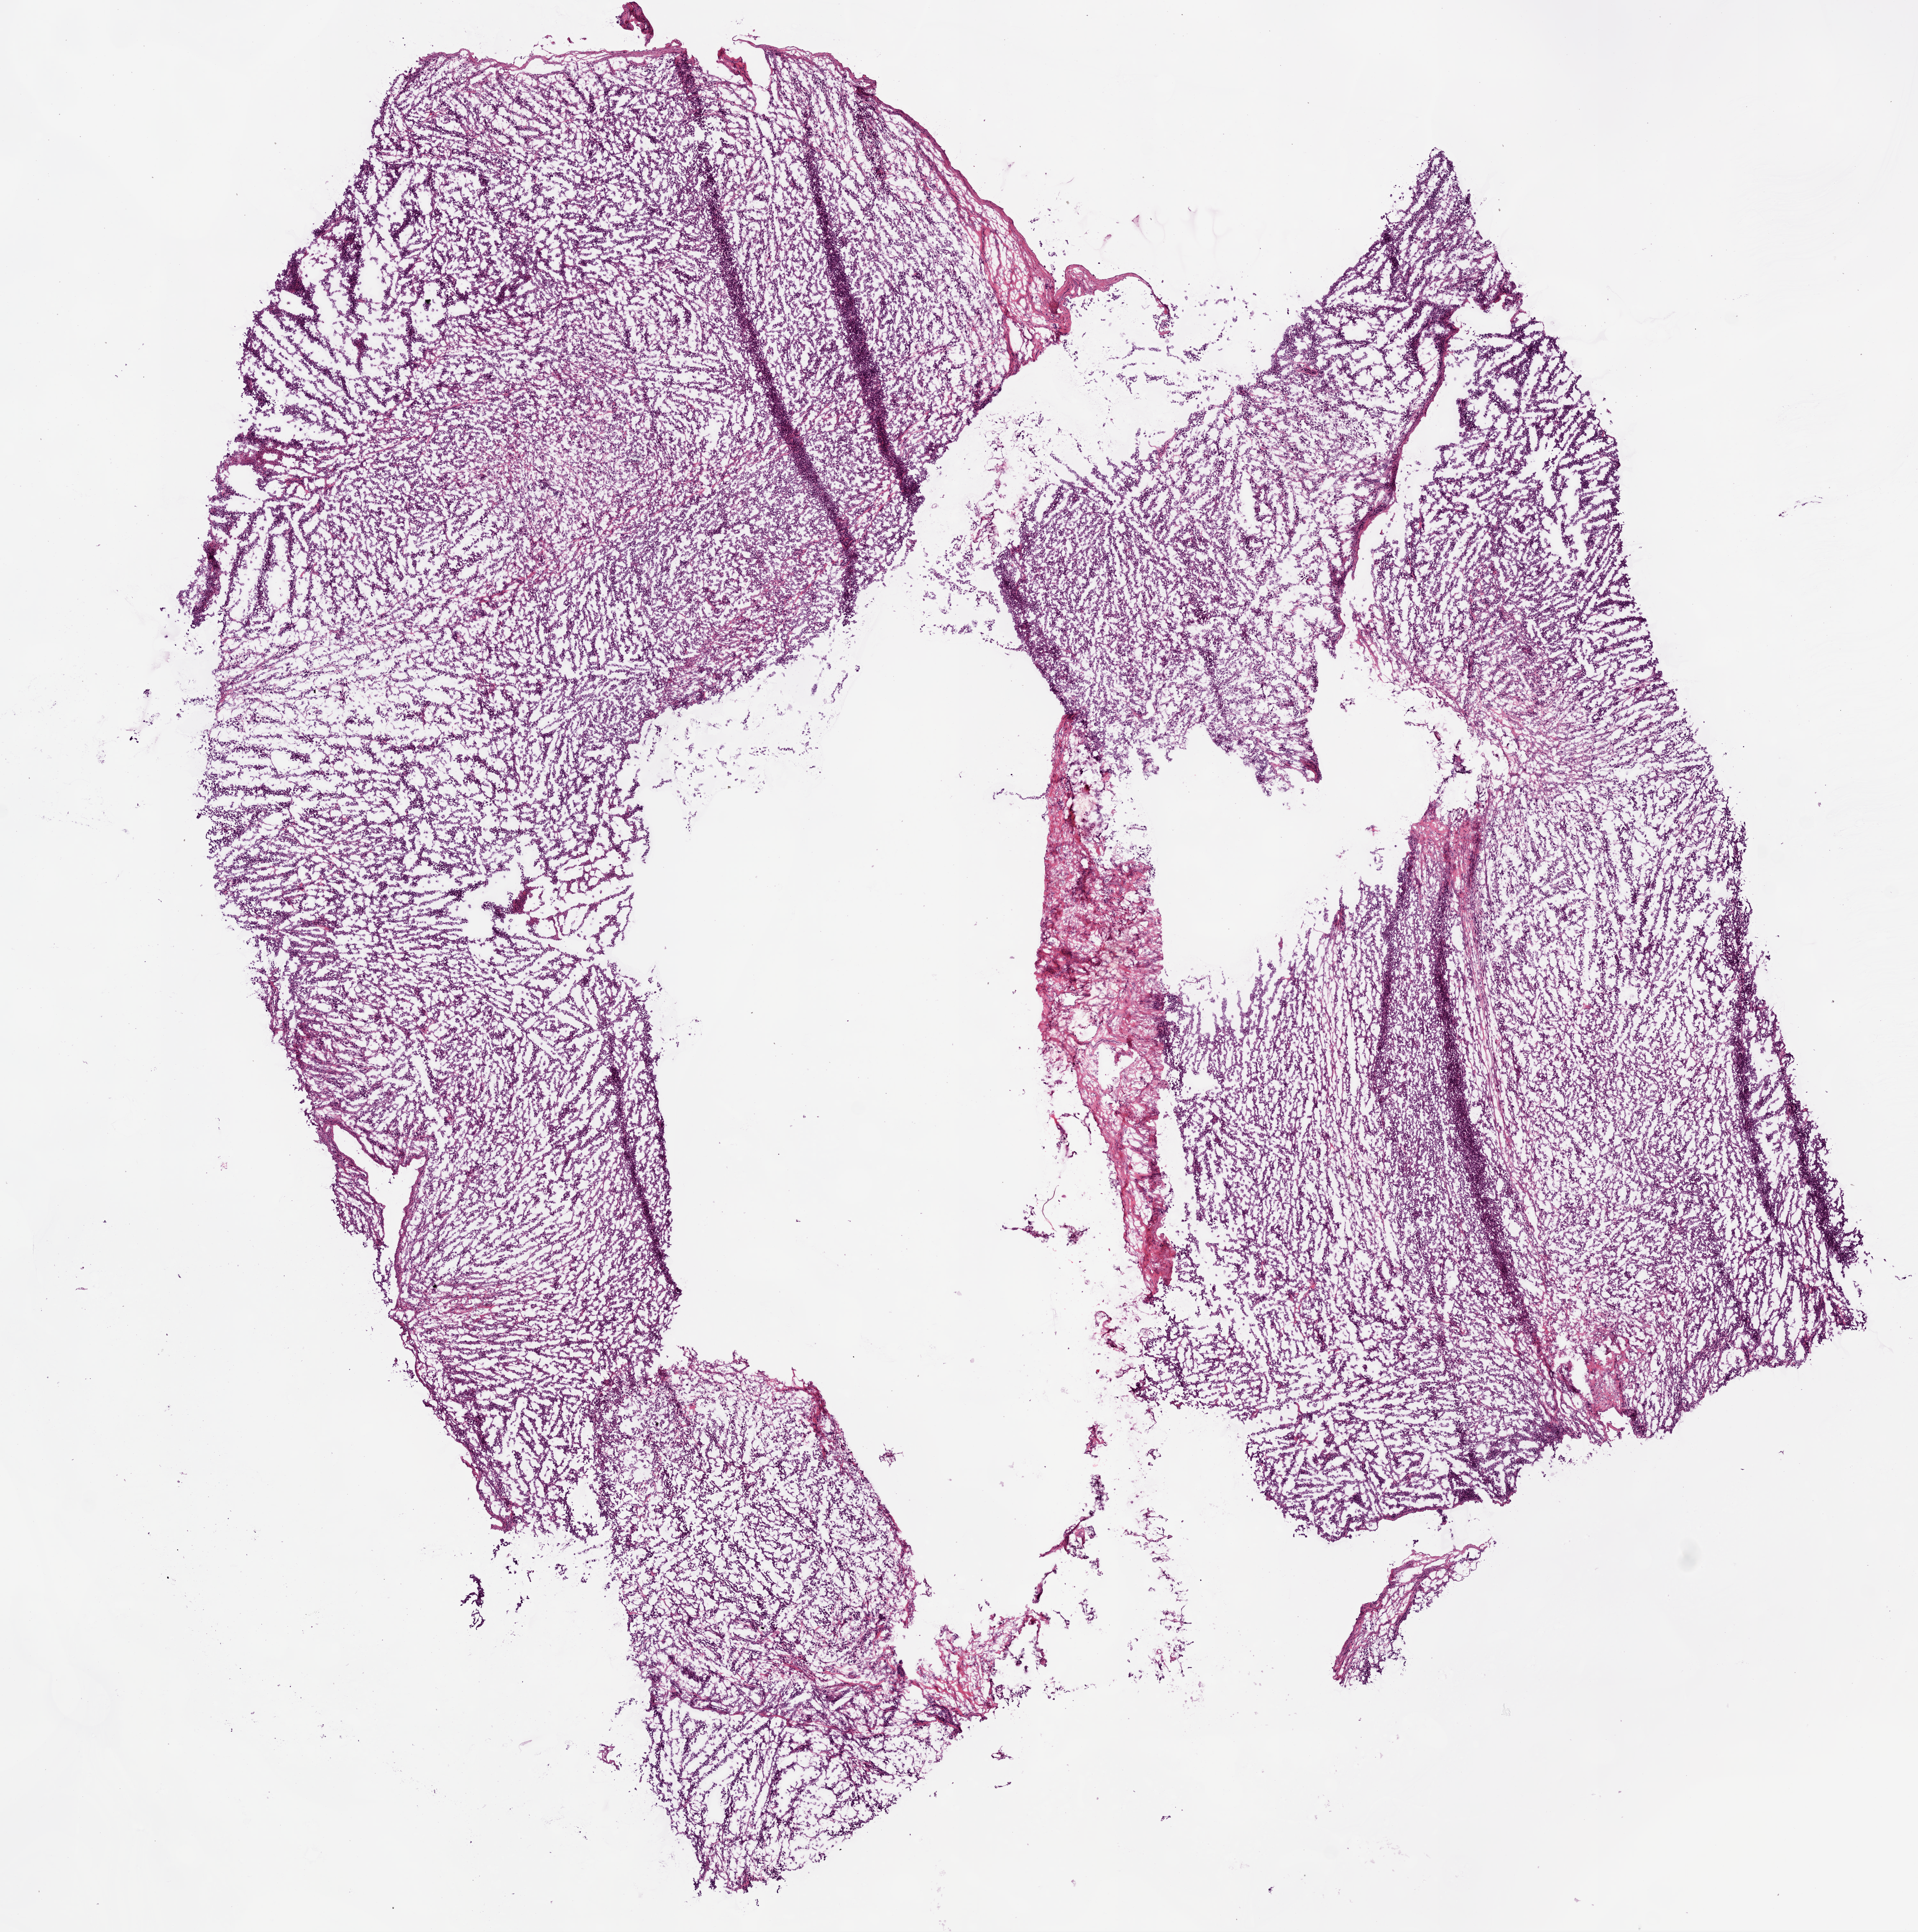
Whole-slide histology image, H&E — a low-resolution overview of the entire scanned area, about 12.0 x 12.1 mm (slide scanned at 20x). Frozen section from the bottom of the tissue portion. Sample: primary tumour, lung. Male patient; age at initial diagnosis 71 years.
Diagnosis: Adenocarcinoma, NOS.